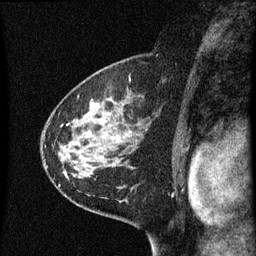
Breast MRI (dynamic contrast-enhanced), one sagittal slice. Dynamic contrast-enhanced series, image 2 of 3 at this slice position (ordered by acquisition). 1.5 T. TE 4.2 ms, TR 8 ms. 2 mm slice thickness. 256 × 256 image matrix. Patient: female, 60 years.
Annotated regions visible in this slice (semi-automatic segmentation, software-assisted and operator-edited):
- analysis volume of interest (the breast-tissue region the enhancement analysis was run in; not a lesion): bounding box [x1, y1, x2, y2] px = [48, 82, 149, 183]
- tumour enhancement mask (voxels above the 70 % enhancement threshold inside the analysis volume of interest): [108, 98, 111, 101]